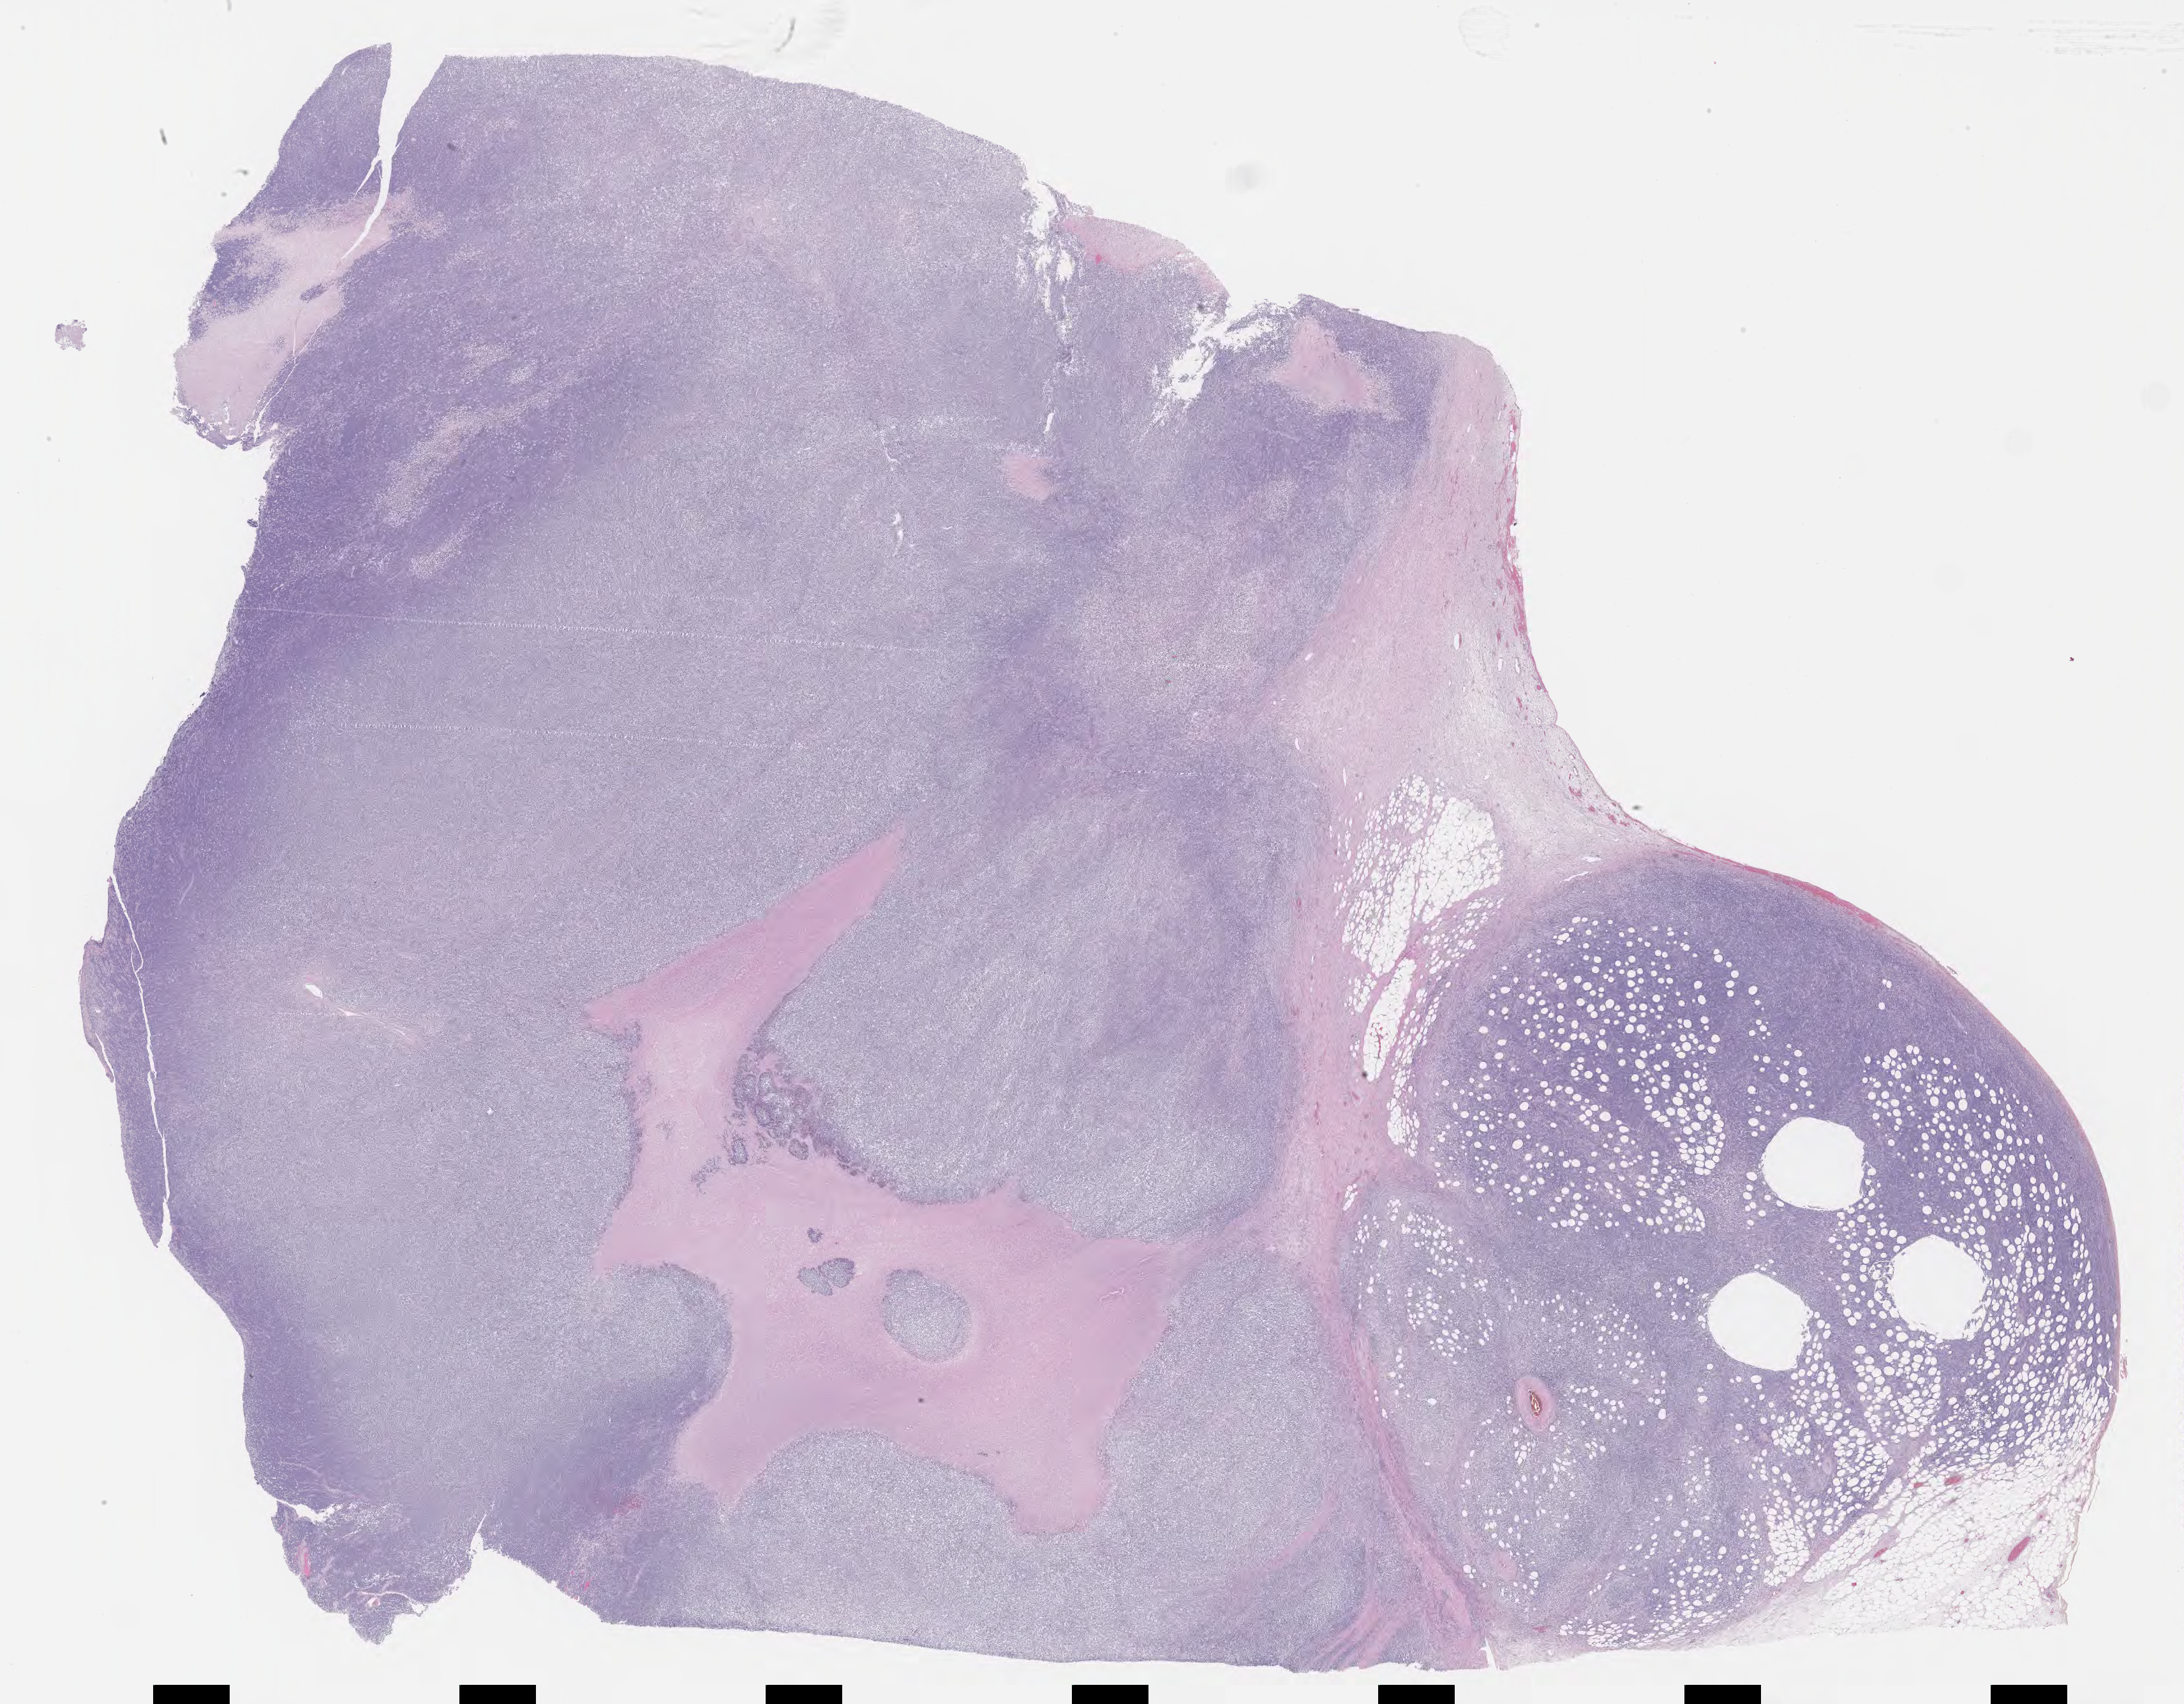
Digitized hematoxylin and eosin (H&E)-stained section — low-resolution overview of the scanned area, about 27.7 x 21.6 mm; tumor tissue; site: small intestine. Patient: male, 59 years old.
Diagnosis: Burkitt lymphoma, NOS.